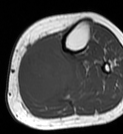
MRI of an extremity soft-tissue mass, one axial slice. Slice 29 of 68 in the series (ordered by position). MR volume resampled by the dataset authors to the PET/CT grid (not the native acquisition matrix). 3.27 mm slice thickness. 123 × 134 image matrix, field of view 120 × 131 mm. Female patient. From the clinical record (not read from this slice): histological type: extraskeletal high grade osteogenic sarcoma; grade: high; site of the primary tumour: left calf.
Outlined on this slice (expert contour drawn on MRI and transferred to this co-registered scan by the dataset authors):
- gross tumour volume (mass): box from (x=20, y=36) to (x=73, y=104) px